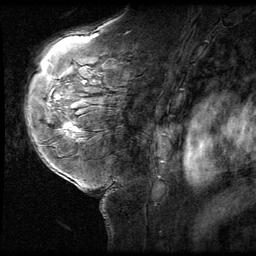
Breast MRI (dynamic contrast-enhanced), one sagittal slice. Position 41 of 58 along the scan axis. 3 images stored at this slice position (order not interpretable as contrast timing). 1.5 T. TE 4.2 ms, TR 9 ms. 256 × 256 image matrix, field of view 180 × 180 mm. Female patient, age 58 years. From the clinical record (not read from this slice): setting: breast cancer imaged before/during neoadjuvant chemotherapy; receptor status: HR-positive, HER2-negative.
Structures marked on this image (semi-automatically segmented with operator editing):
- analysis volume of interest (the breast-tissue region the enhancement analysis was run in; not a lesion): bounding box <51,116,93,151> (left, top, right, bottom; pixels)
- tumour enhancement mask (voxels above the 140 % enhancement threshold inside the analysis volume of interest): <64,124,81,131>